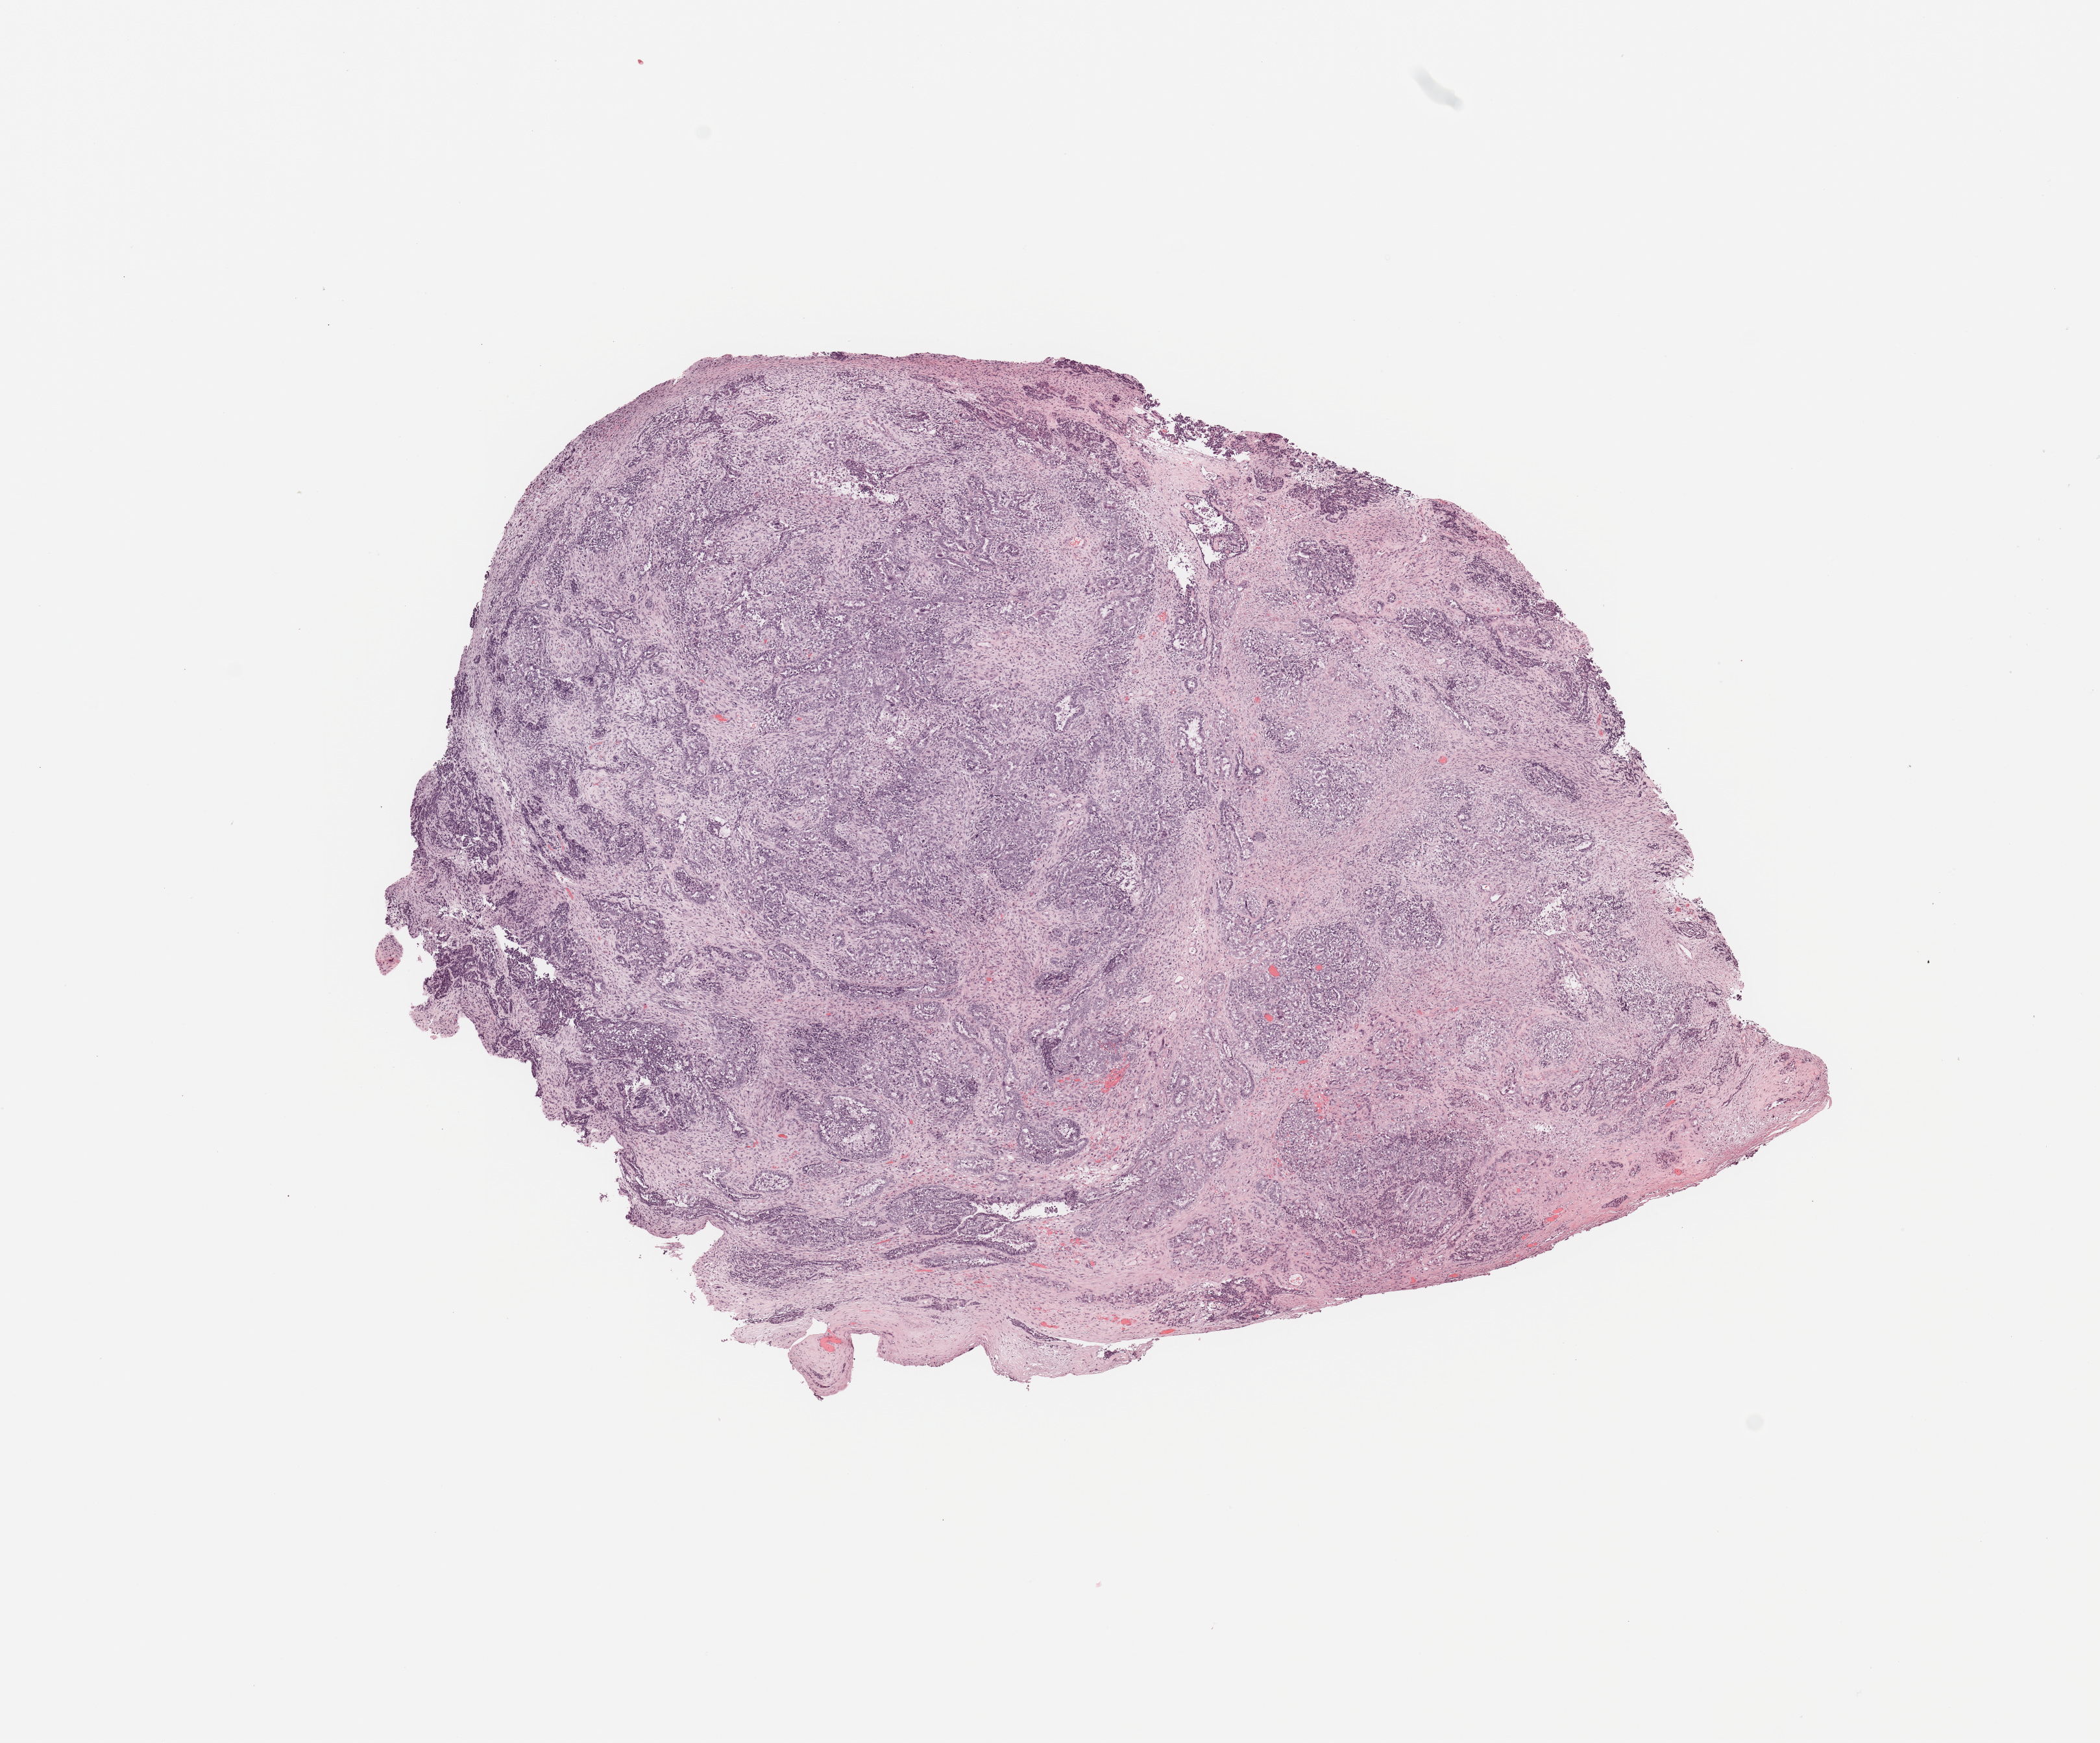
Digitized H&E-stained tissue section (whole slide) — shown as a low-resolution overview of the whole scanned area (about 12.8 x 10.6 mm); tumour tissue sample, sampled site: uterus. 61-year-old female patient. Histologic grade: G3 (poorly differentiated). Pathologist review of this section (percent, as recorded): tumour nuclei 80%, necrosis 0%.
Histologic diagnosis: Endometrioid adenocarcinoma, NOS. AJCC pathologic stage: IV.